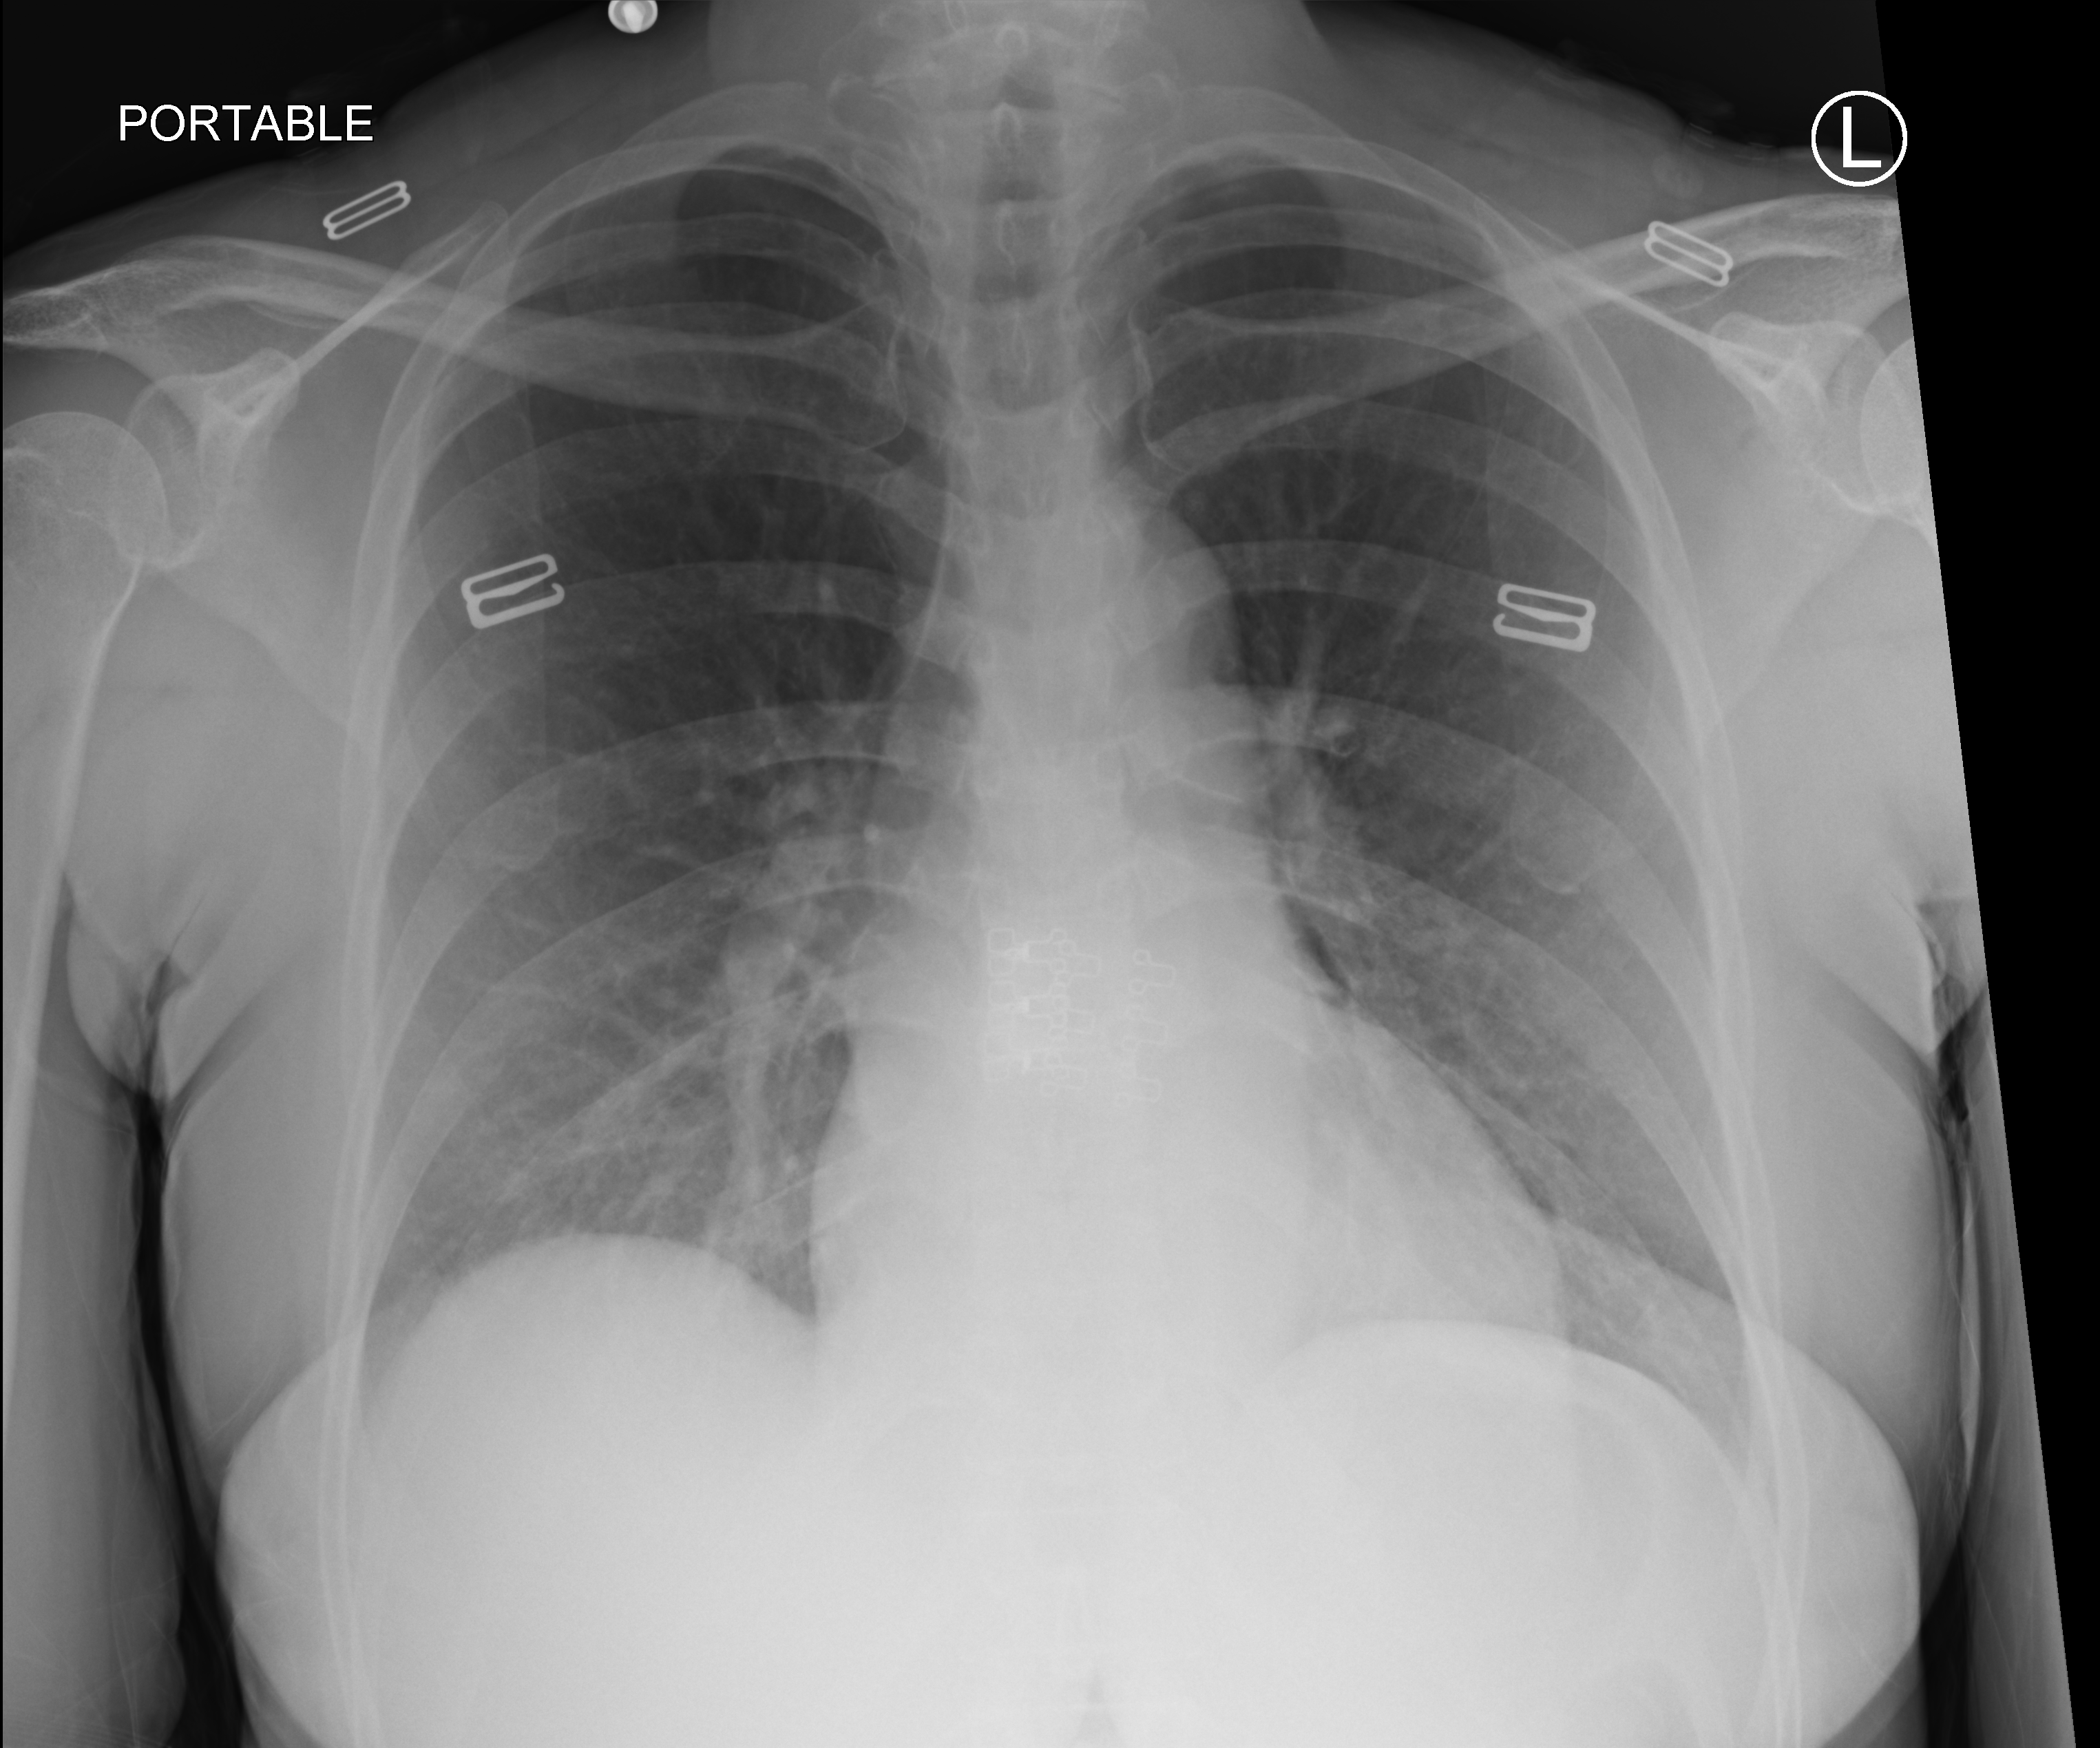
Chest X-ray (portable); anteroposterior (AP) projection. Female patient hospitalised with COVID-19, age 18–59 years.
From the hospital-stay record, not from the radiograph (when in the stay this image was taken is not recorded): other chronic lung disease (admission record): no; length of hospital stay: 2 days; admitted to intensive care during this hospital stay: no.